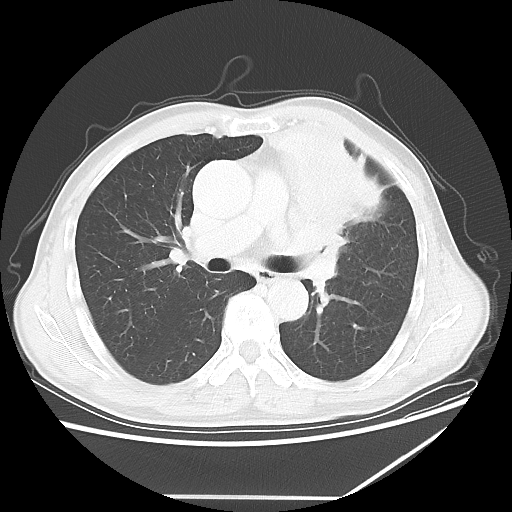
Chest CT, one axial slice. Position 37 of 64 along the scan axis. Reconstruction kernel LUNG. 100 kVp. Lung window (W 1500 / L -600 HU). 512 × 512 image matrix. Male patient, age 64 years. From the clinical record (not read from this slice): clinical TNM (as recorded): T1c N1 M1.
Outlined on this slice (rectangle marked by the reading radiologist):
- lung tumour (recorded histology: squamous cell carcinoma): bounding box <269,123,452,312> (left, top, right, bottom; pixels)